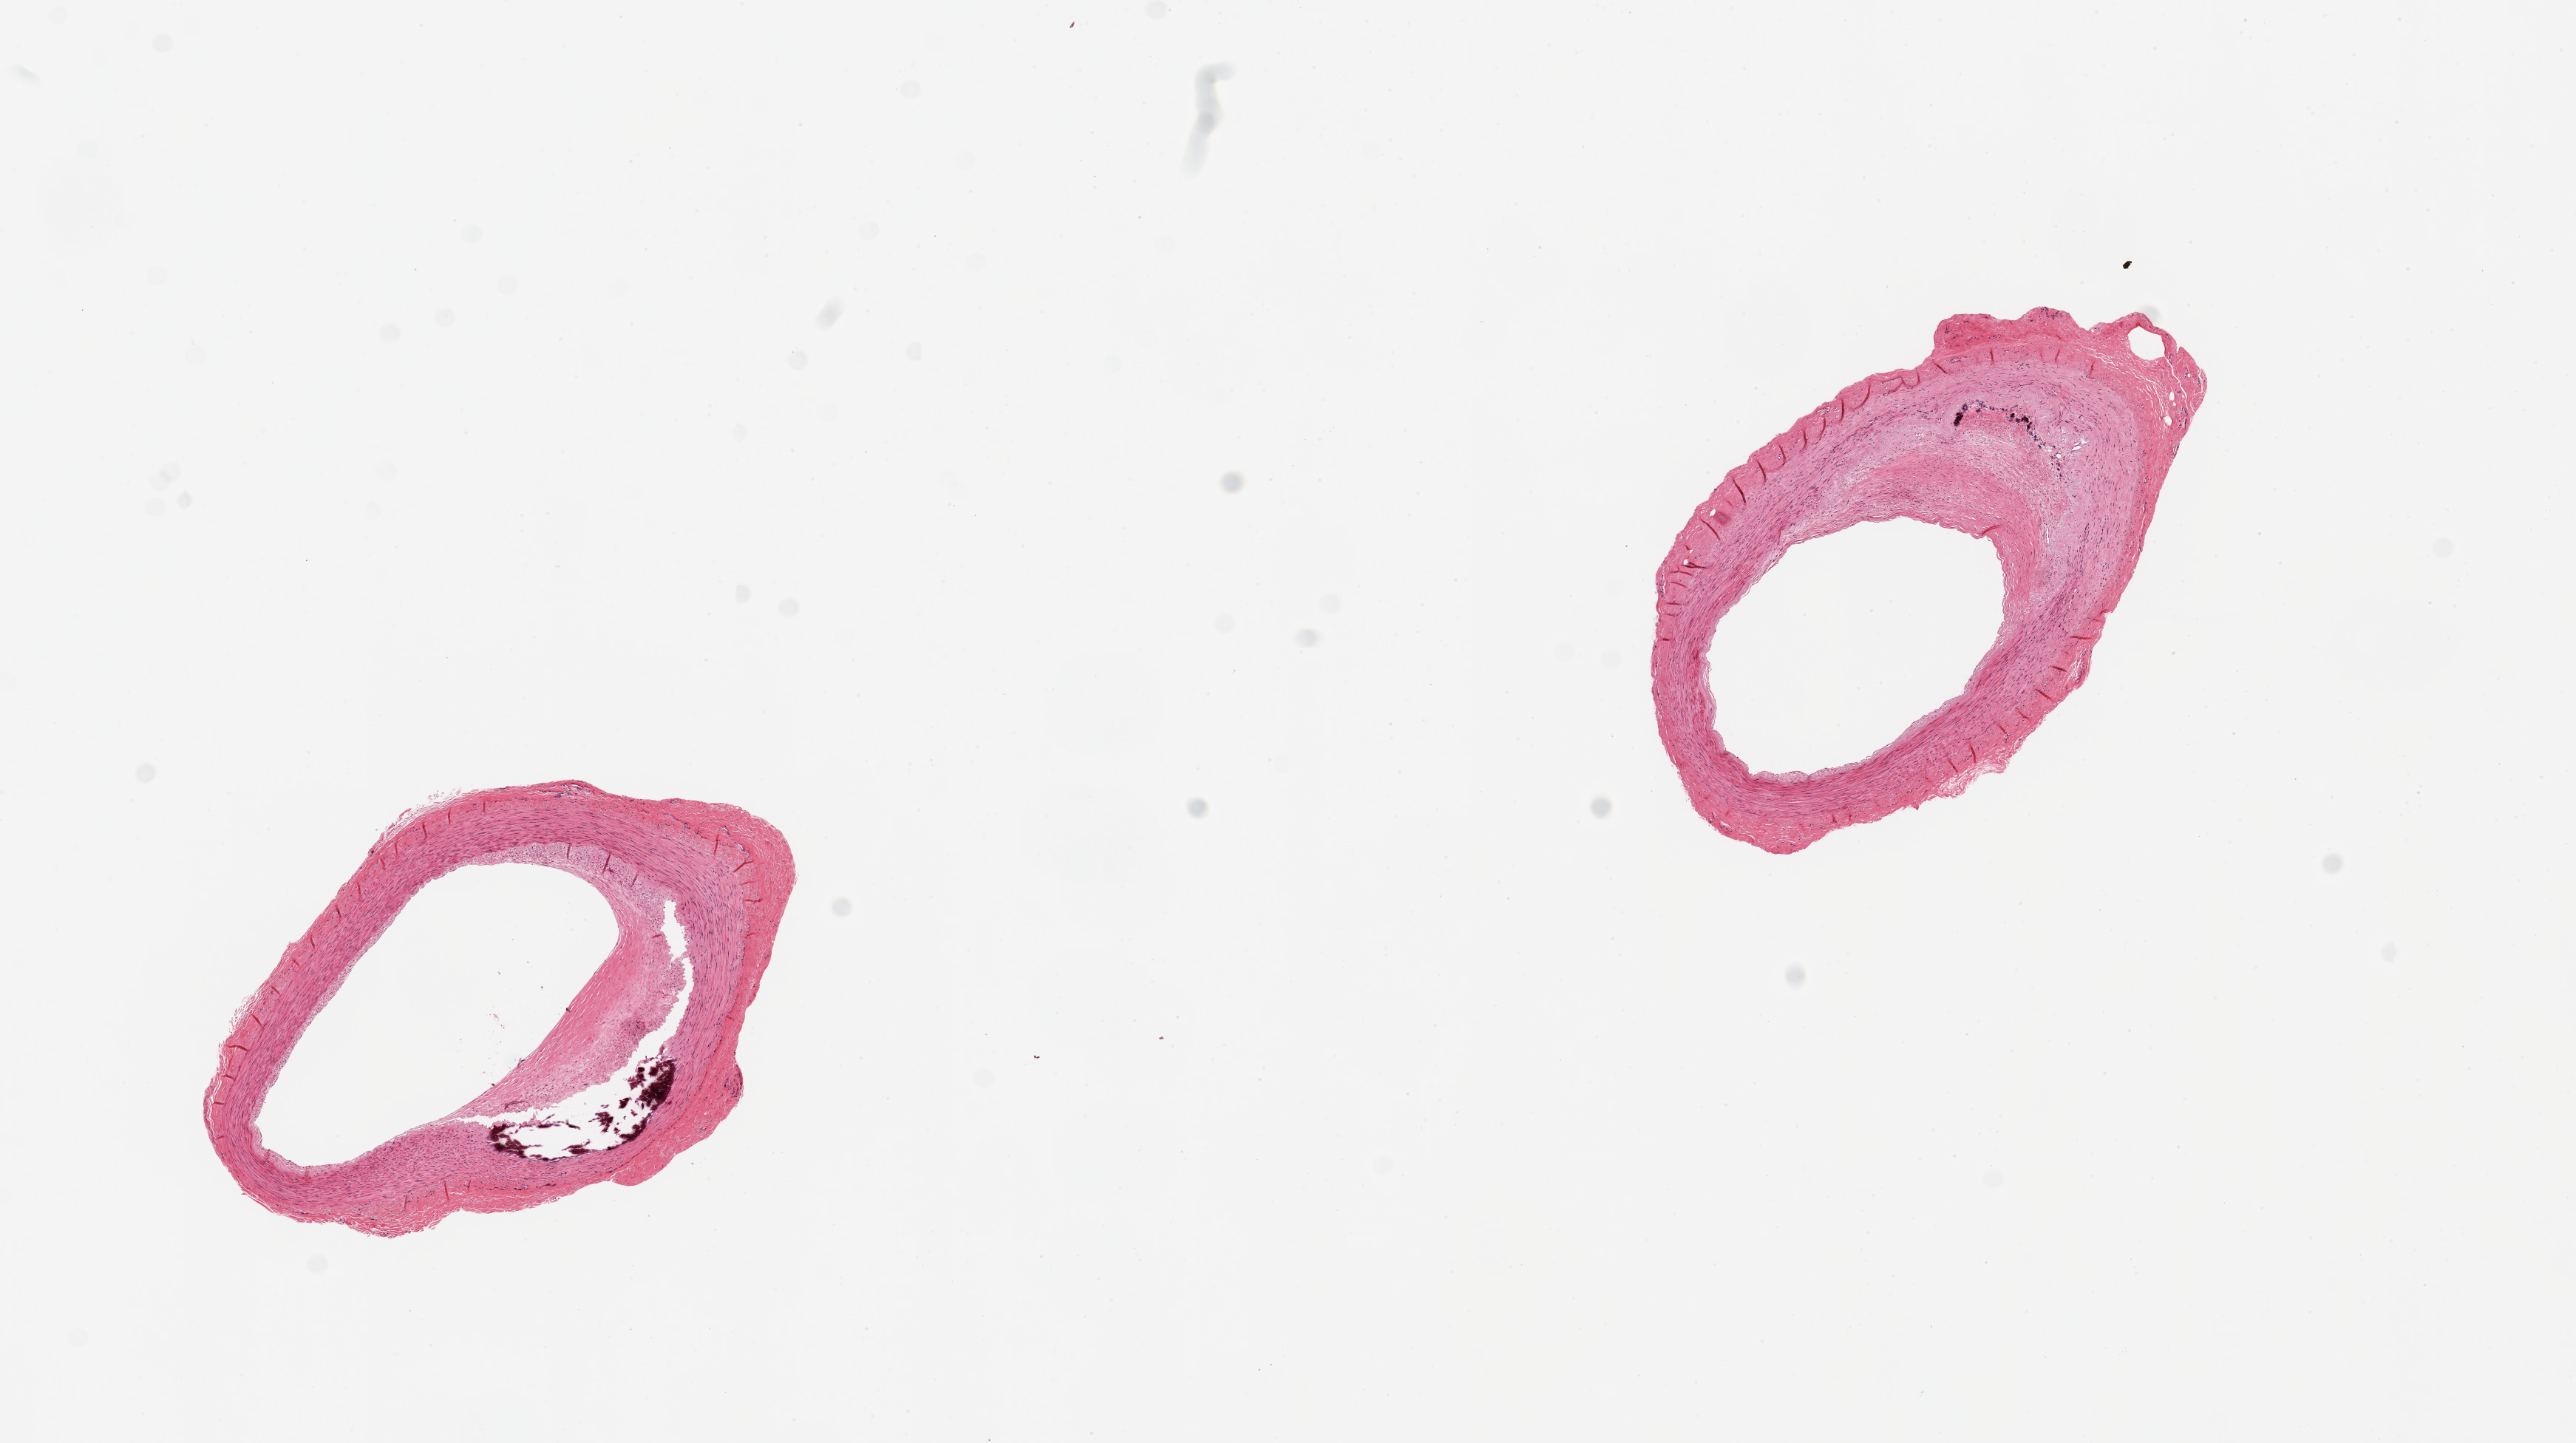
Whole-slide image, haematoxylin and eosin stain, brightfield, low-resolution overview of the scanned area, about 13.8 x 7.7 mm (from a 20x scan). PAXgene-fixed paraffin-embedded (PFPE) section. Sampled site (target tissue): tibial artery. Donor tissue sample. Donor: female.
Reviewer comment on this tissue sample: 2 pieces; calcified plaques.